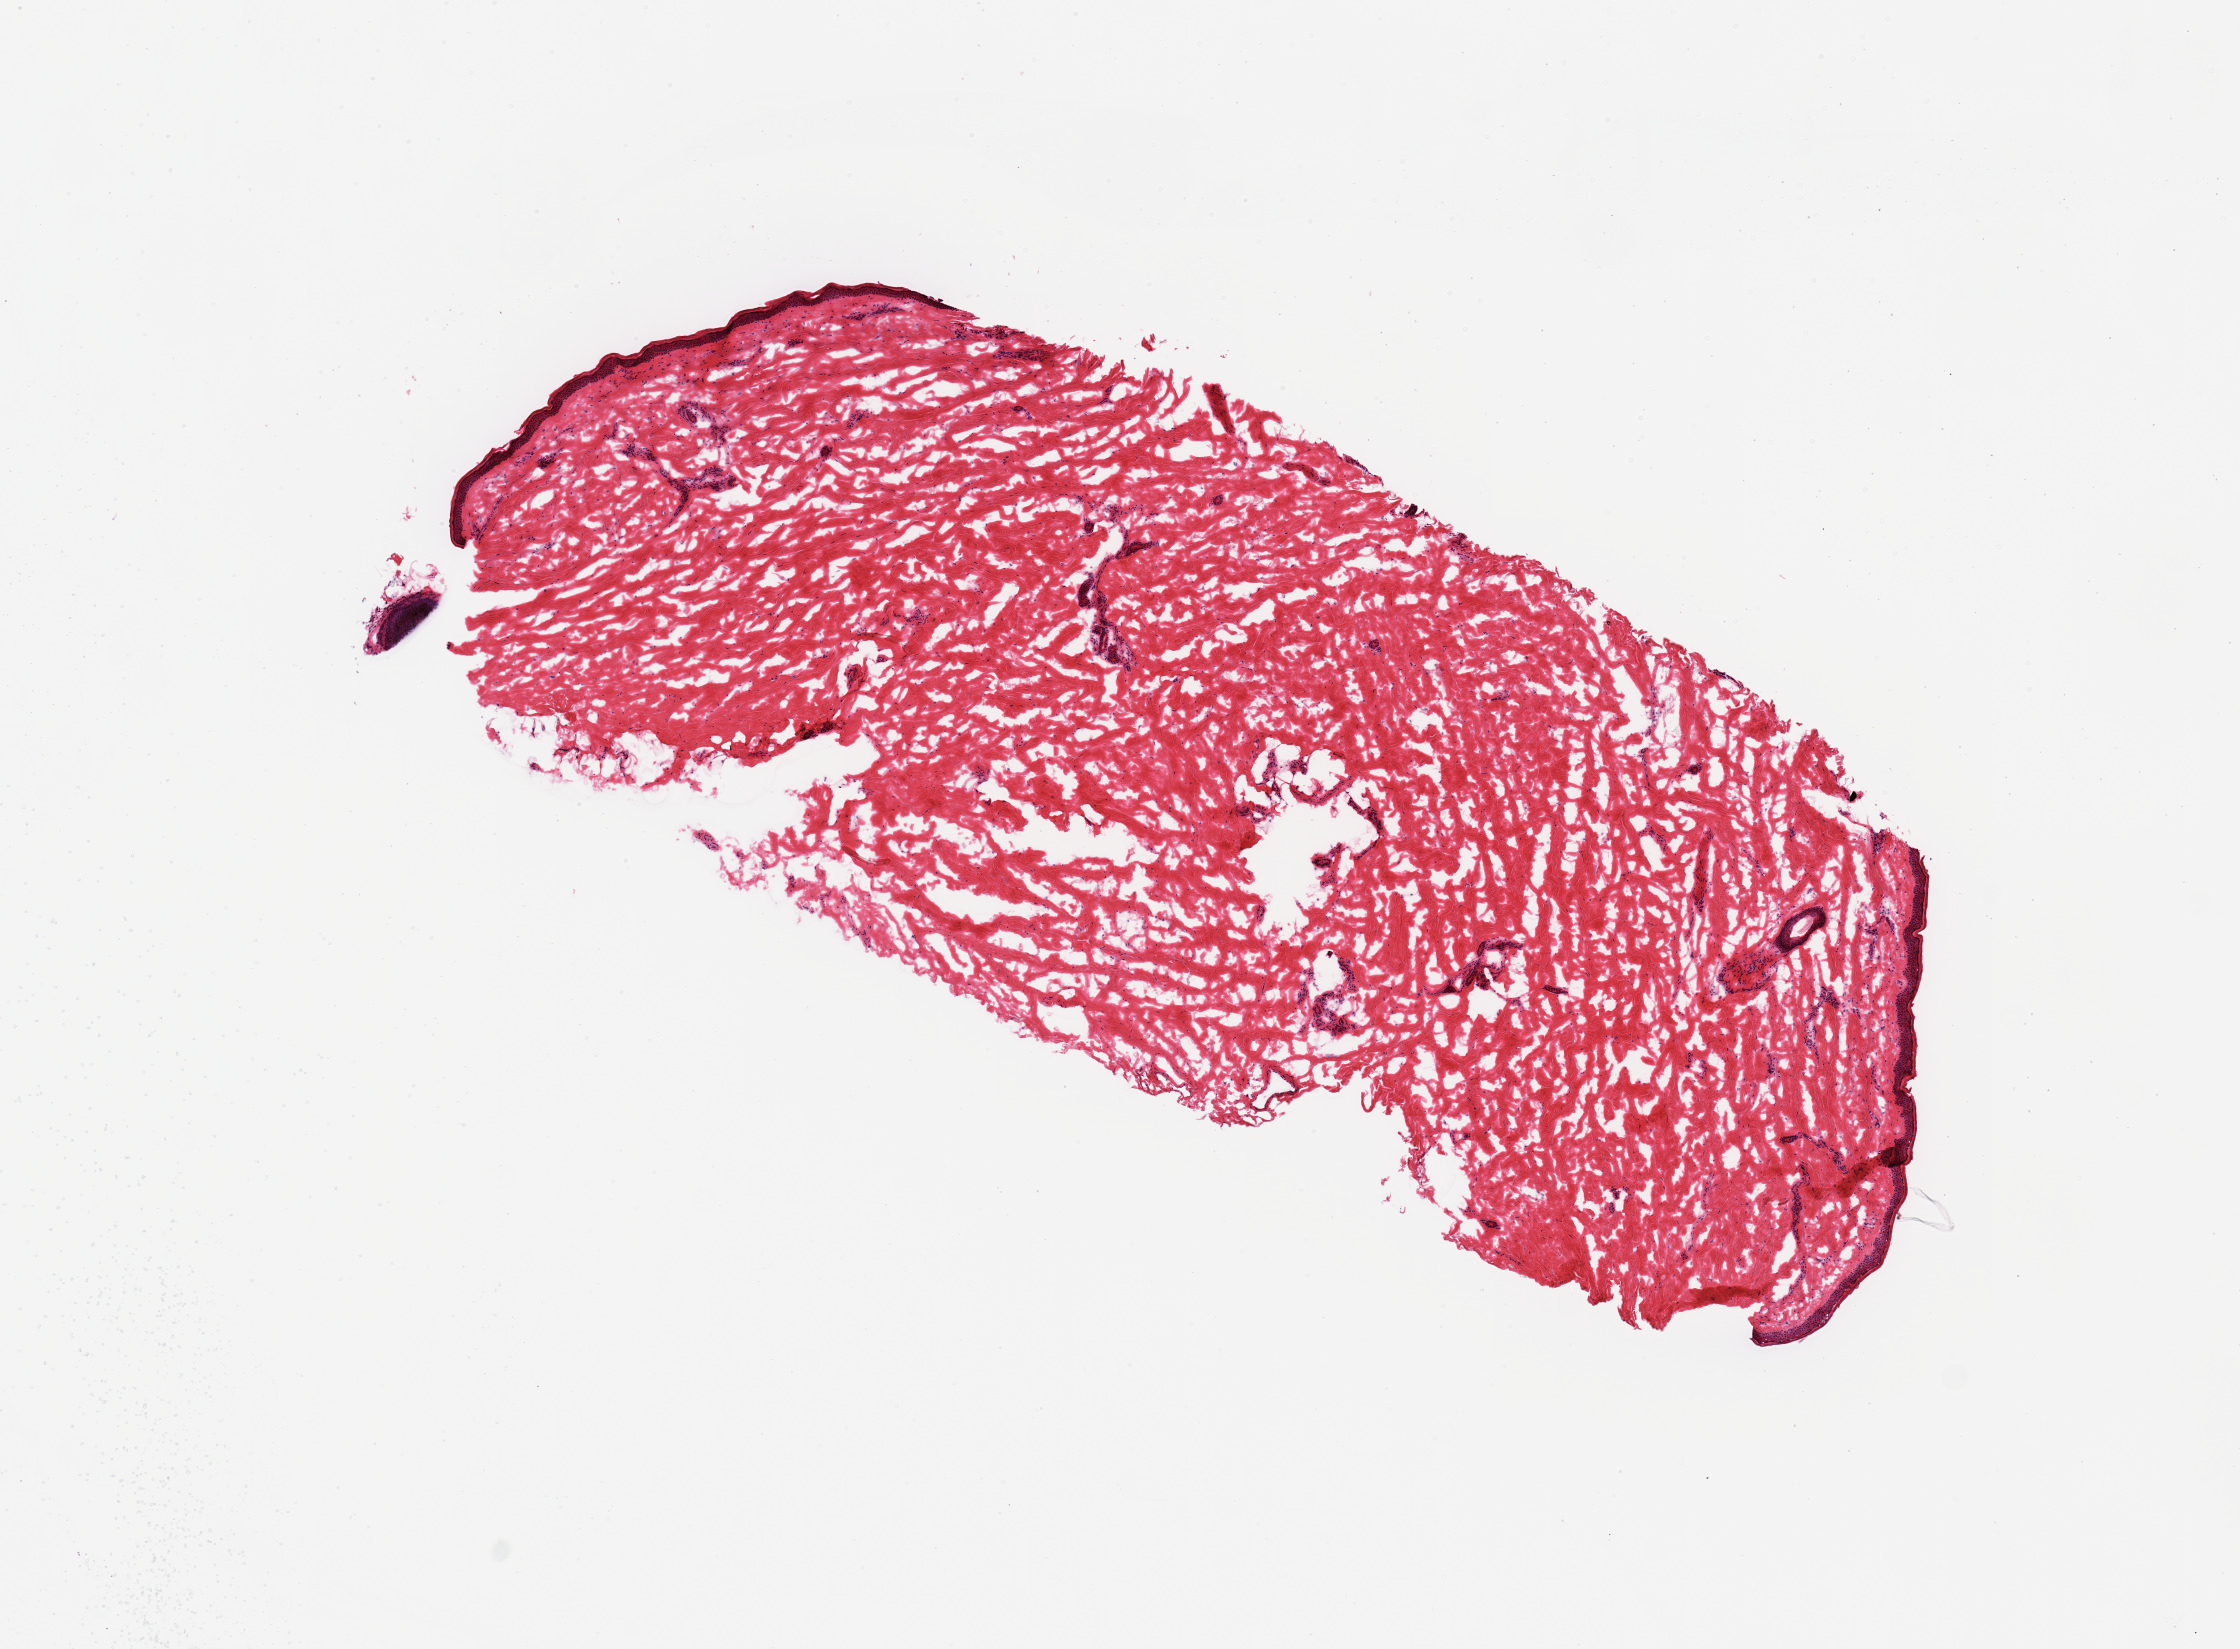
Digitized hematoxylin and eosin (H&E)-stained section, brightfield — a low-resolution overview of the entire scanned area, about 8.9 x 6.5 mm (slide scanned at 20x). Frozen section. Section of skin of lower leg (target tissue). Donor tissue sample. Male donor.
Pathologist's review note for this sample: 1 piece.